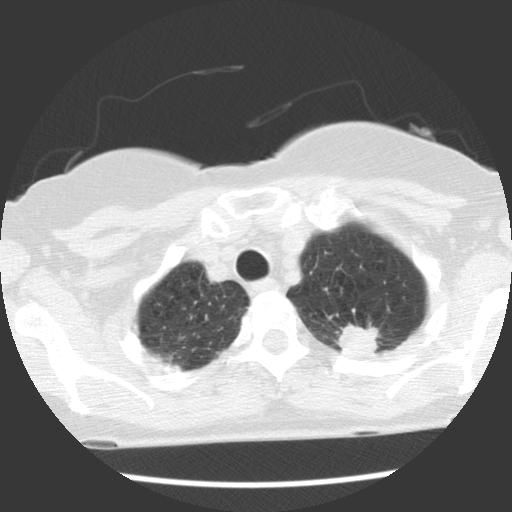
Low-dose screening chest CT, one axial slice. Position 101 of 120 along the scan axis. Reconstruction kernel STANDARD. 140 kVp. Lung window (W 1500 / L -600 HU). 2.5 mm slice thickness. 512 × 512 image matrix, field of view 300 × 300 mm.
Annotated regions visible in this slice (outlined manually by an expert reader):
- lesion 1 (tumor, upper lobe of left lung): bounding box <336,324,380,358> (left, top, right, bottom; pixels)